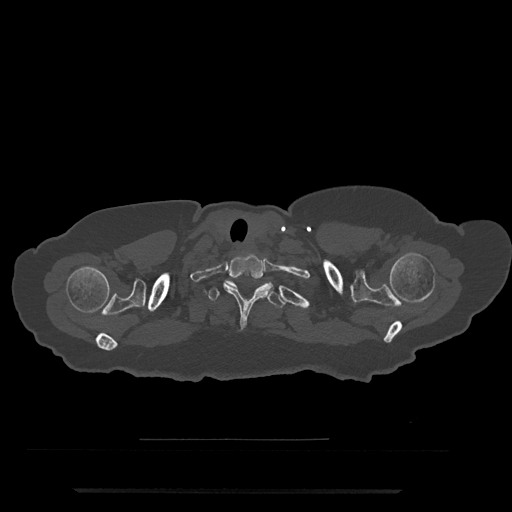
CT including the spine, one axial slice. Slice 699 of 797 in the series (ordered by position). 120 kVp. Bone window (W 1800 / L 400 HU). 0.5 mm slice thickness. 512 × 512 image matrix, field of view 440 × 440 mm. Patient: female, 51 years. From the clinical record (not read from this slice): primary cancer: neuro; vertebrae with lytic lesions (as recorded): T8.
Structures marked on this image (semi-automatic segmentation, software-assisted and operator-edited):
- T1 vertebra: bounding box <223,254,273,328> (left, top, right, bottom; pixels)
- T2 vertebra: <209,279,286,309>